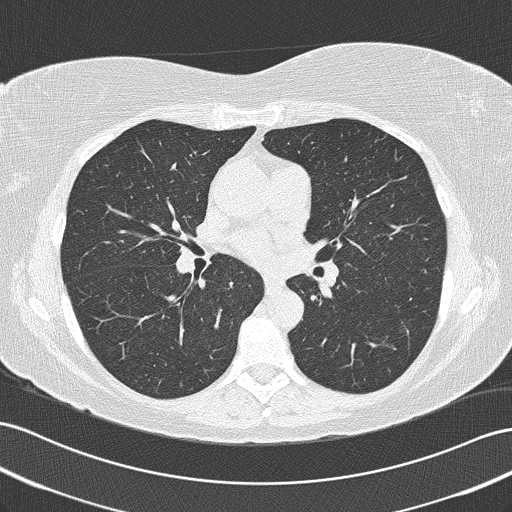
Chest CT (low-dose screening protocol), one axial image; first (baseline) screen; lung window (W 1500 / L -600 HU); slice 84 of 172 in the series. Female, age 57 years at enrolment.
Expert reader's lesion annotation, box from (x=384, y=310) to (x=431, y=351) px. Screening reader's record for this exam (one nodule recorded; not confirmed to be the boxed lesion): non-calcified nodule or mass ≥4 mm, left lower lobe, 11 × 11 mm, spiculated (stellate) margins, ground glass attenuation. Official screen result: positive, change unspecified: nodule(s) >= 4 mm or enlarging nodule(s), mass(es), or other non-specific abnormalities suspicious for lung cancer.